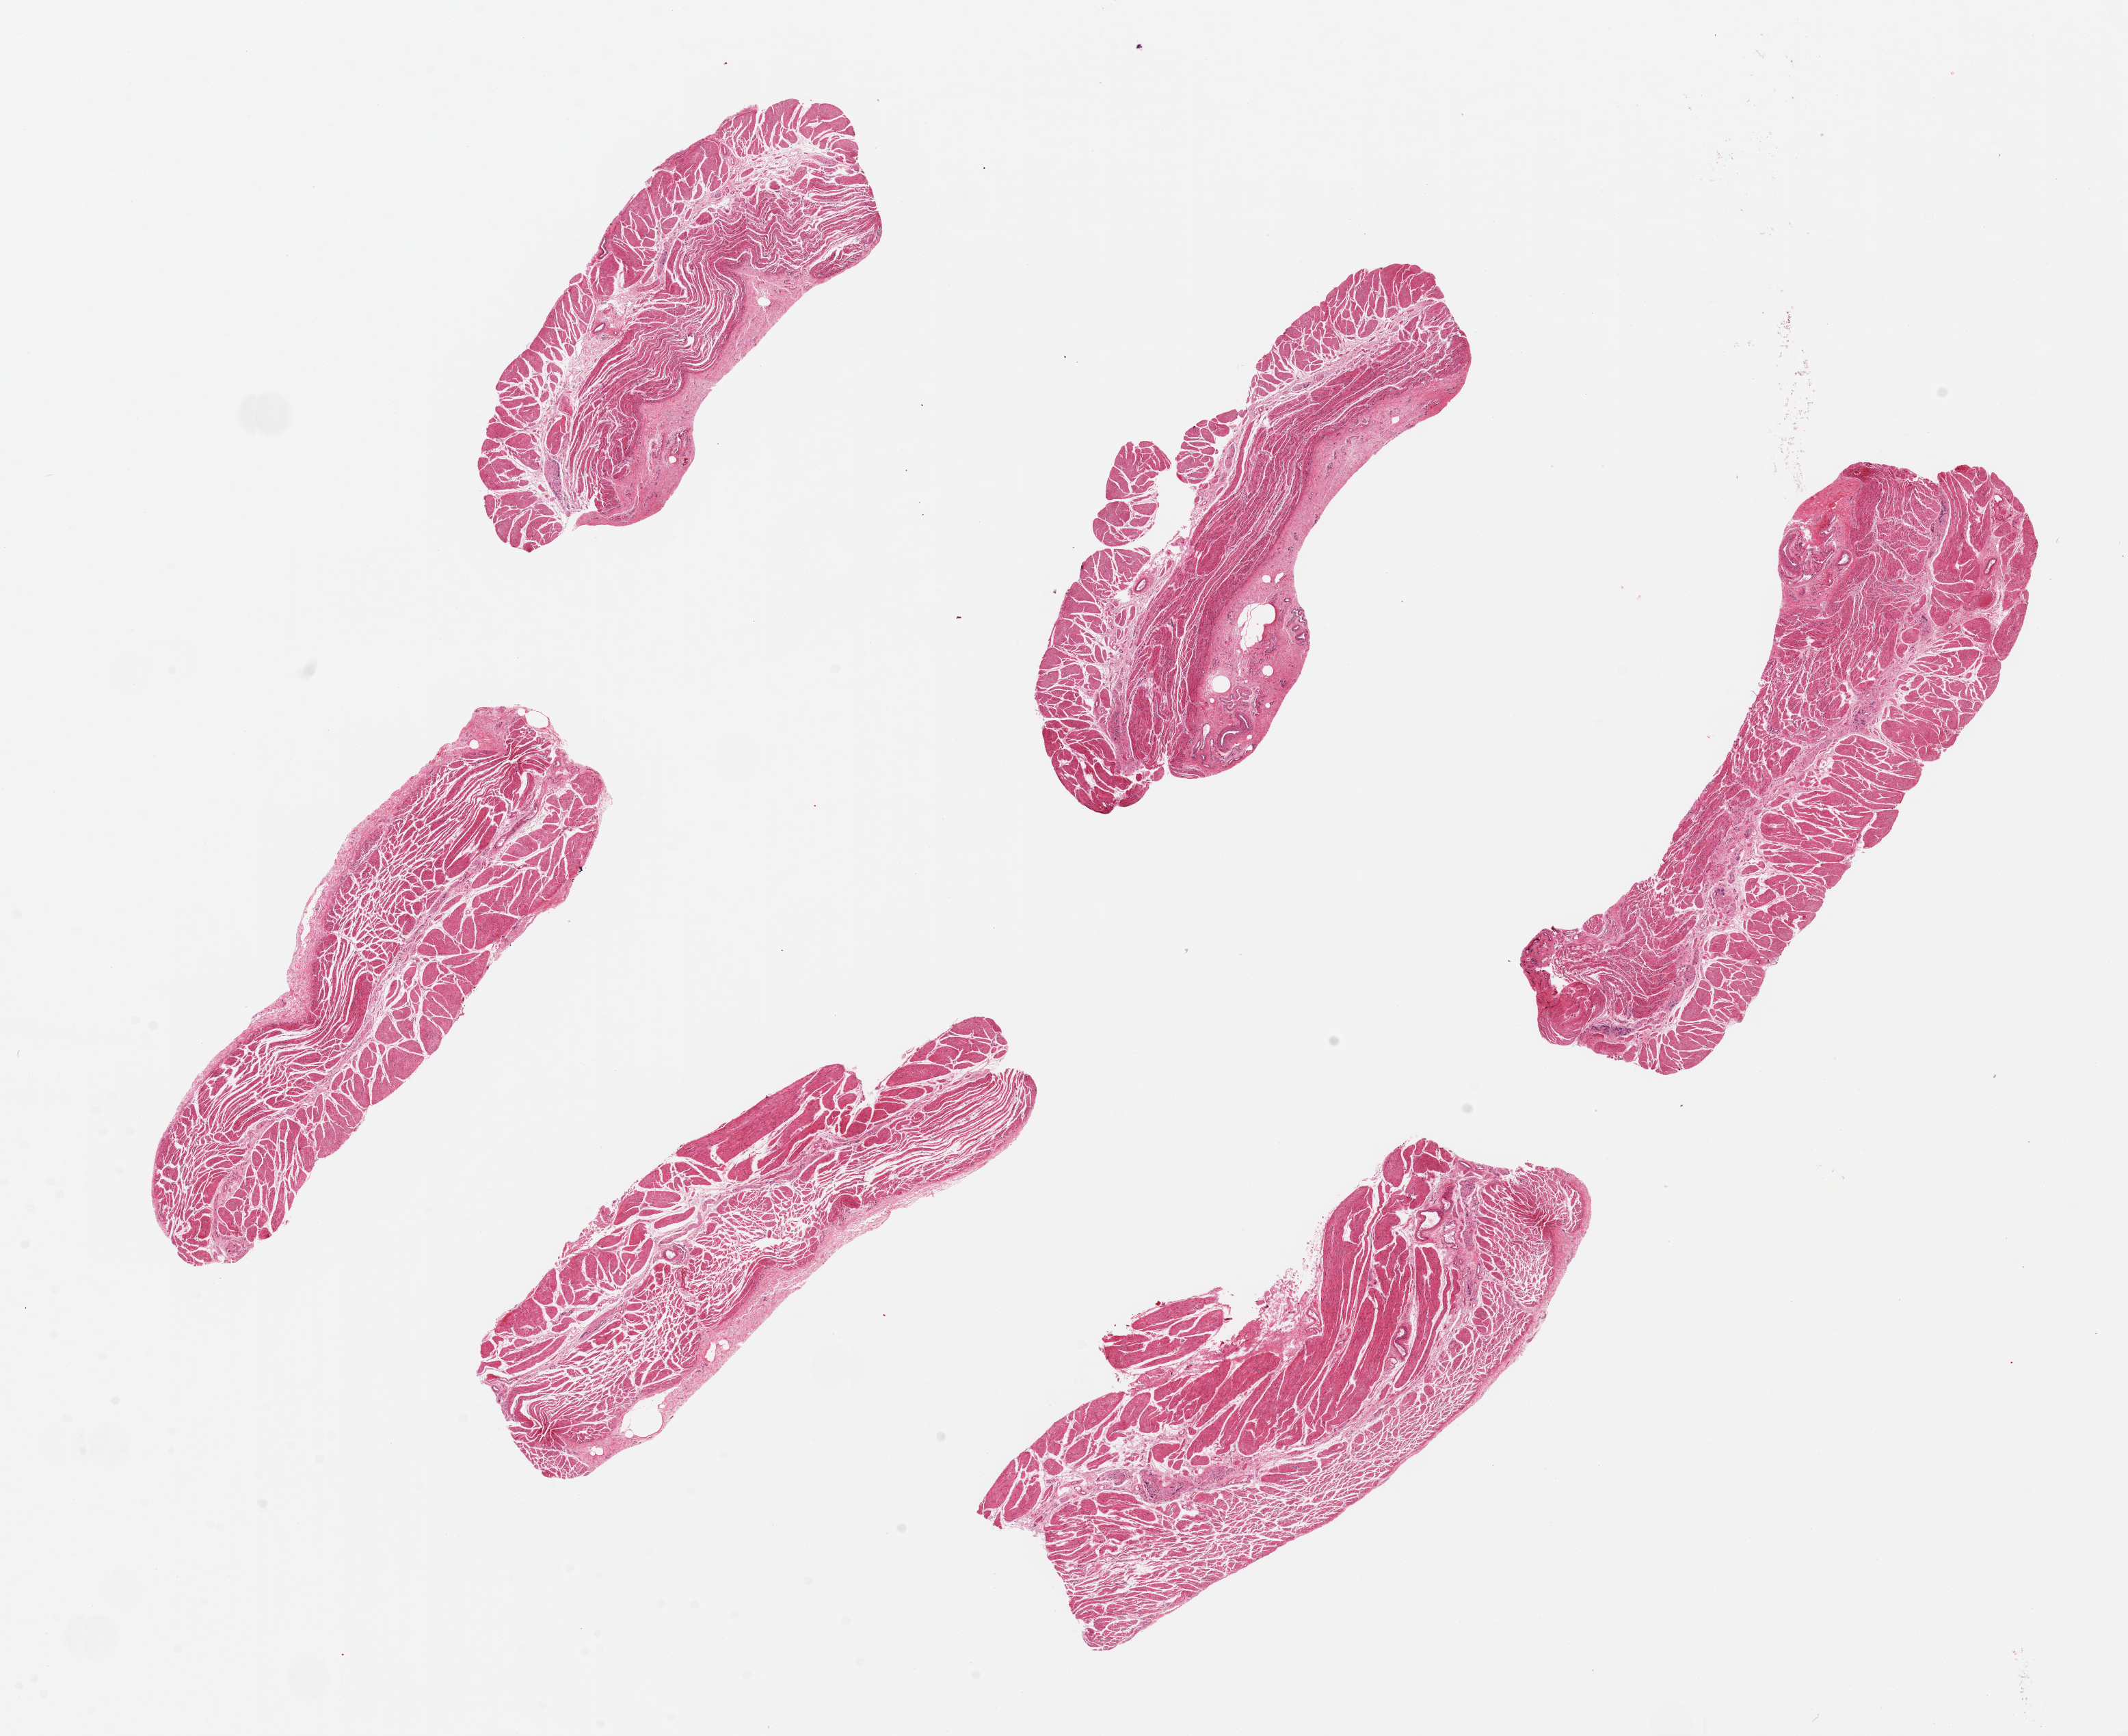
Digitized H&E-stained section — low-resolution overview of the scanned area, about 24.6 x 20.1 mm; PAXgene-fixed, paraffin-embedded tissue; target tissue: esophageal muscle; tissue donor sample. Female donor.
* pathologist's review note for this sample: 6 pieces, up to 8x3mm; all muscle; well preserved neurons